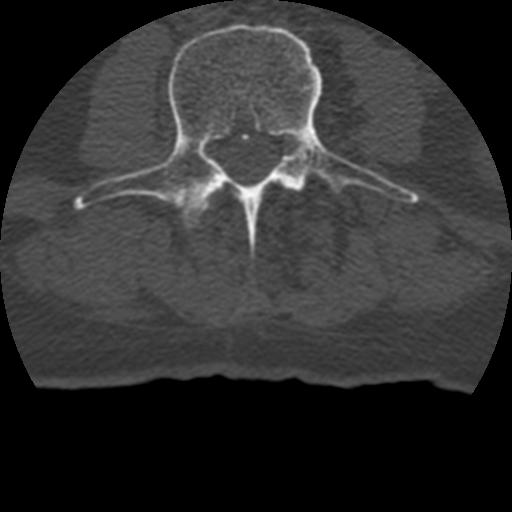
CT including the spine, one axial slice. Position 92 of 399 along the scan axis. Reconstruction kernel STANDARD. 120 kVp. Bone window (W 1800 / L 400 HU). 512 × 512 image matrix. Patient age 69 years. From the clinical record (not read from this slice): primary cancer: prostate.
Structures marked on this image (semi-automatically segmented with operator editing):
- L3 vertebra: box from (x=77, y=23) to (x=413, y=228) px